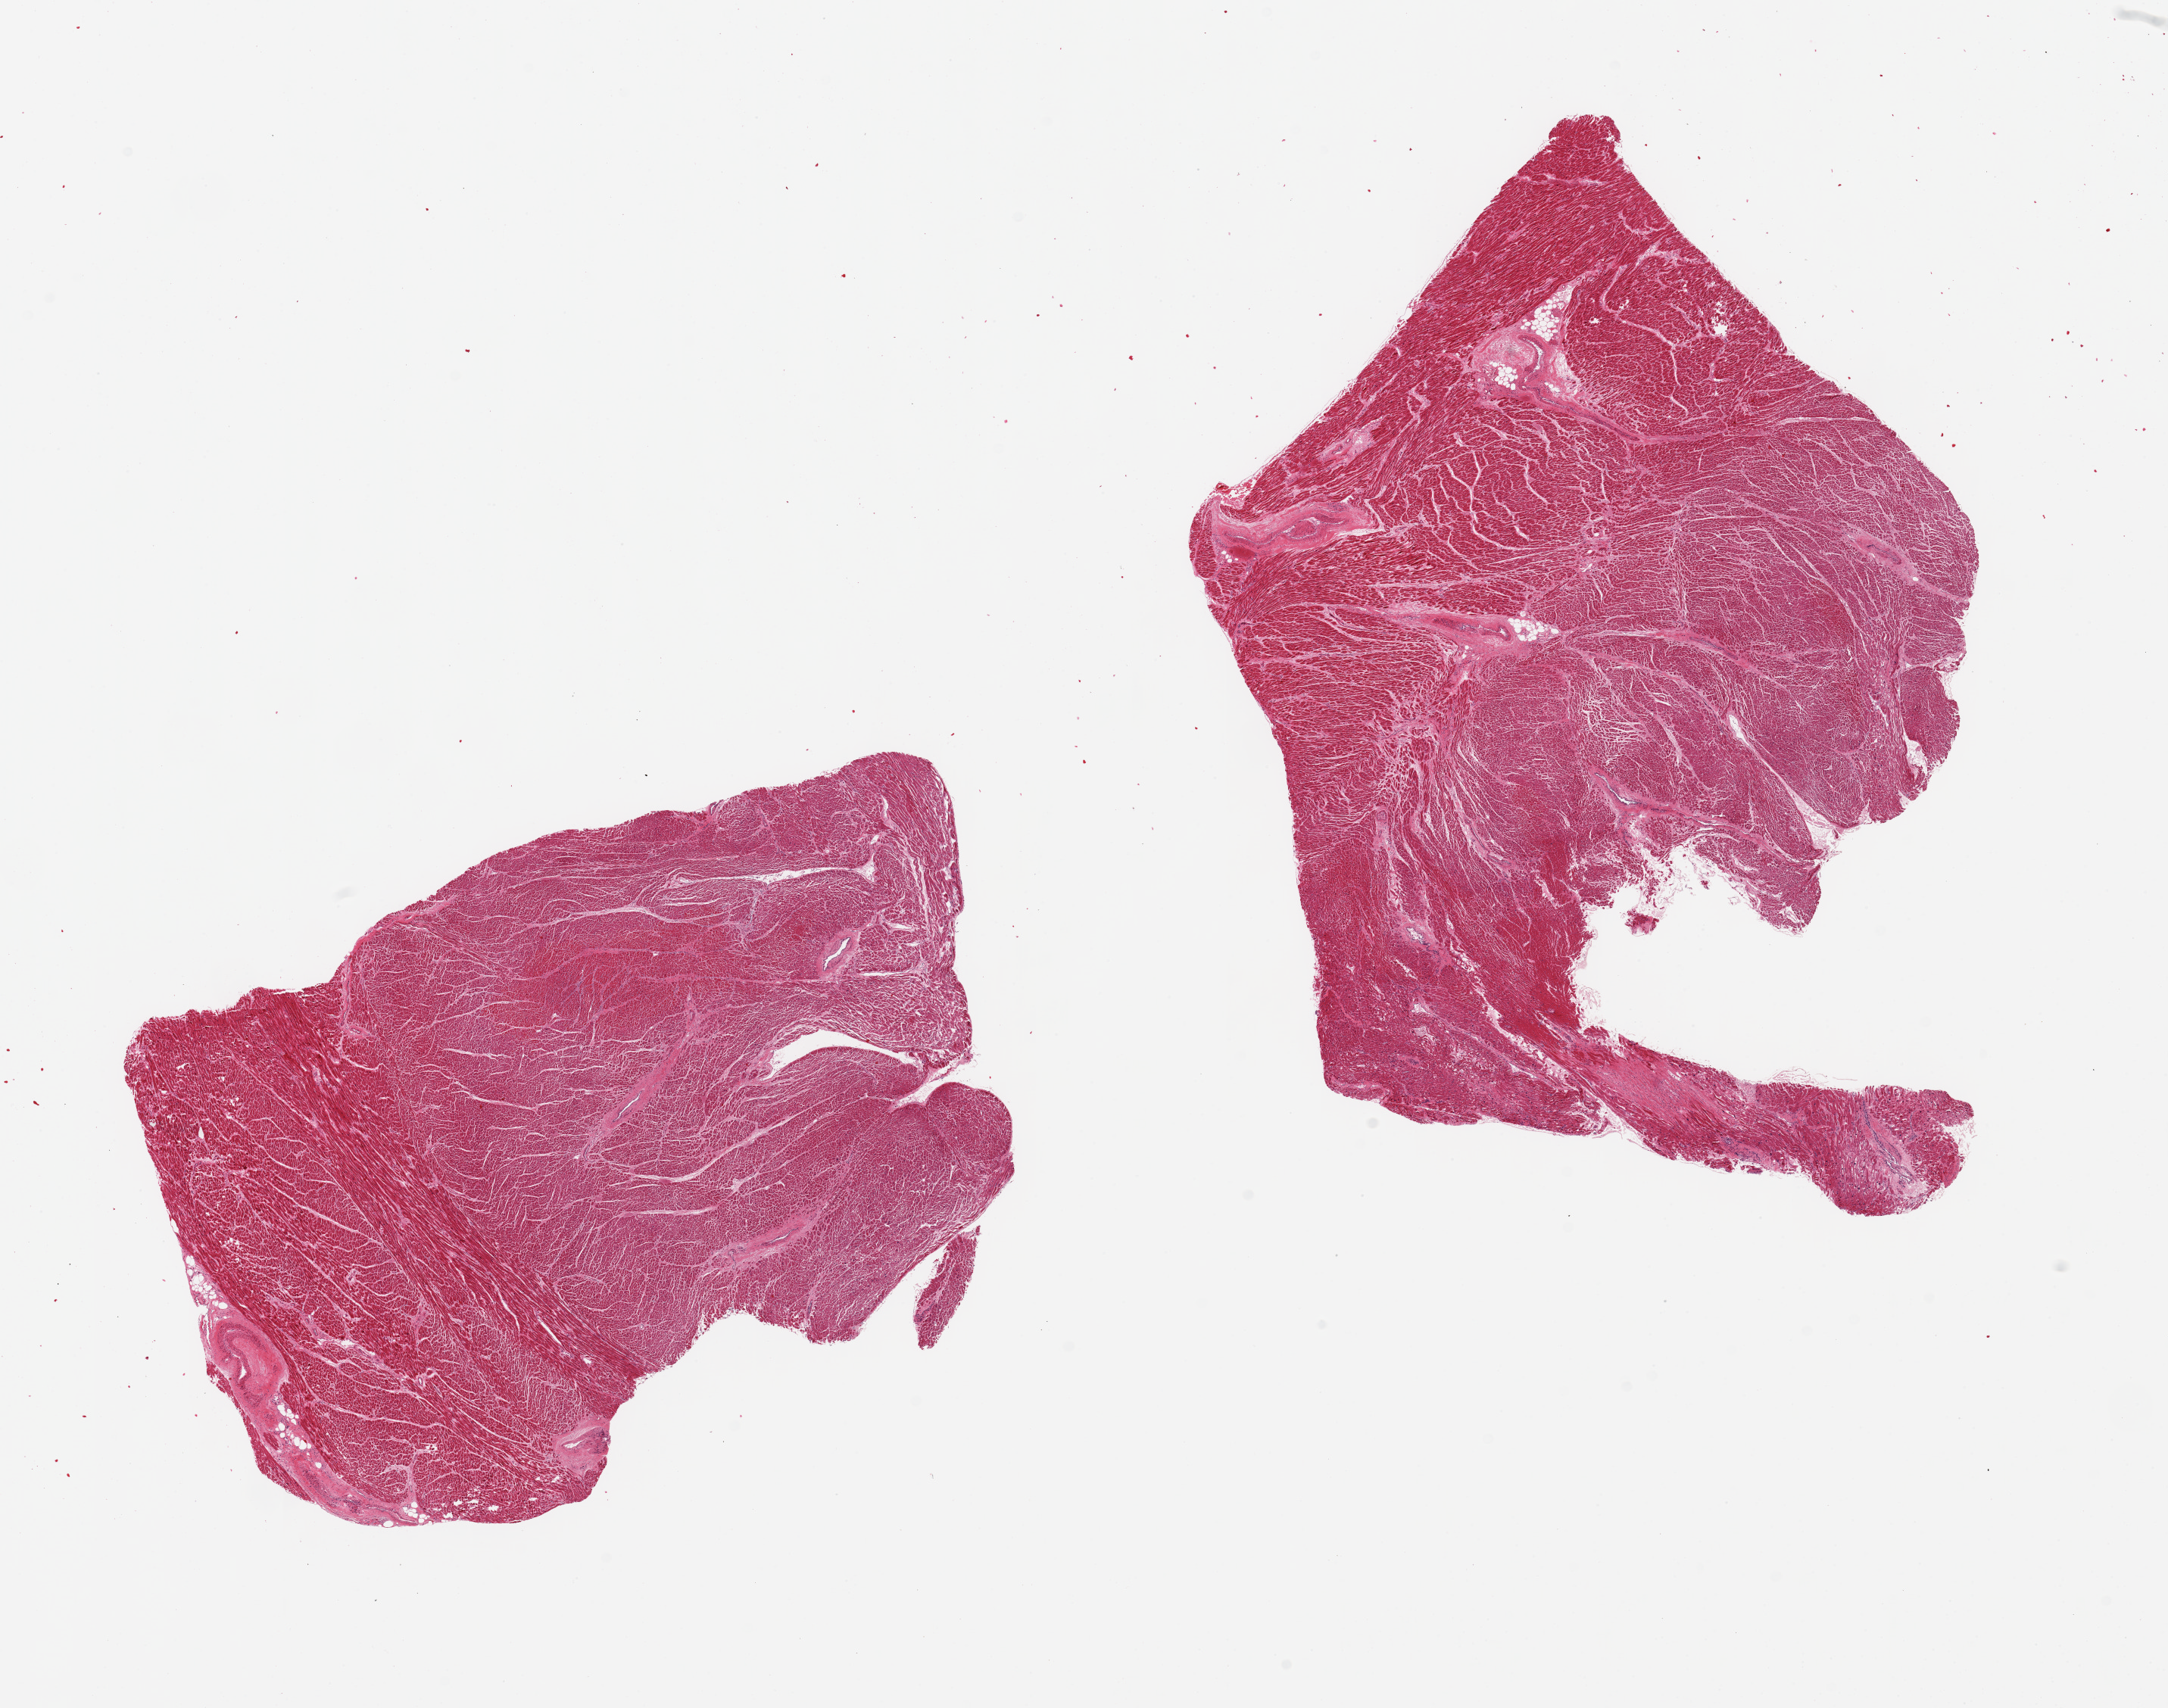
Digitized hematoxylin and eosin (H&E)-stained section — a low-resolution overview of the entire scanned area, about 22.6 x 17.8 mm (slide scanned at 20x). PAXgene-fixed, paraffin-embedded tissue. Sampled site (target tissue): heart. Donor tissue sample. Male donor.
Review note (as recorded): 2 pieces; interstitial and patchy fibrosis with foci of hypereosinophilia and influx of neutrophils consistent with acute myocardial infarction.